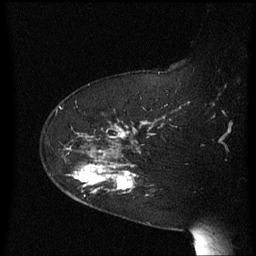
Breast MRI (dynamic contrast-enhanced), one sagittal slice; position 46 of 60 along the scan axis; dynamic contrast-enhanced series, image 2 of 3 at this slice position (ordered by acquisition); 1.5 T; TE 4.2 ms, TR 8.4 ms; 2.3 mm slice thickness; 256 × 256 image matrix. Female patient, age 63 years. From the clinical record (not read from this slice): setting: breast cancer imaged before/during neoadjuvant chemotherapy; receptor status: HER2-positive.
Annotated regions visible in this slice (semi-automatically segmented with operator editing):
- analysis volume of interest (the breast-tissue region the enhancement analysis was run in; not a lesion): bounding box <64,144,142,206> (left, top, right, bottom; pixels)
- tumour enhancement mask (voxels above the 70 % enhancement threshold inside the analysis volume of interest): <72,164,136,192>